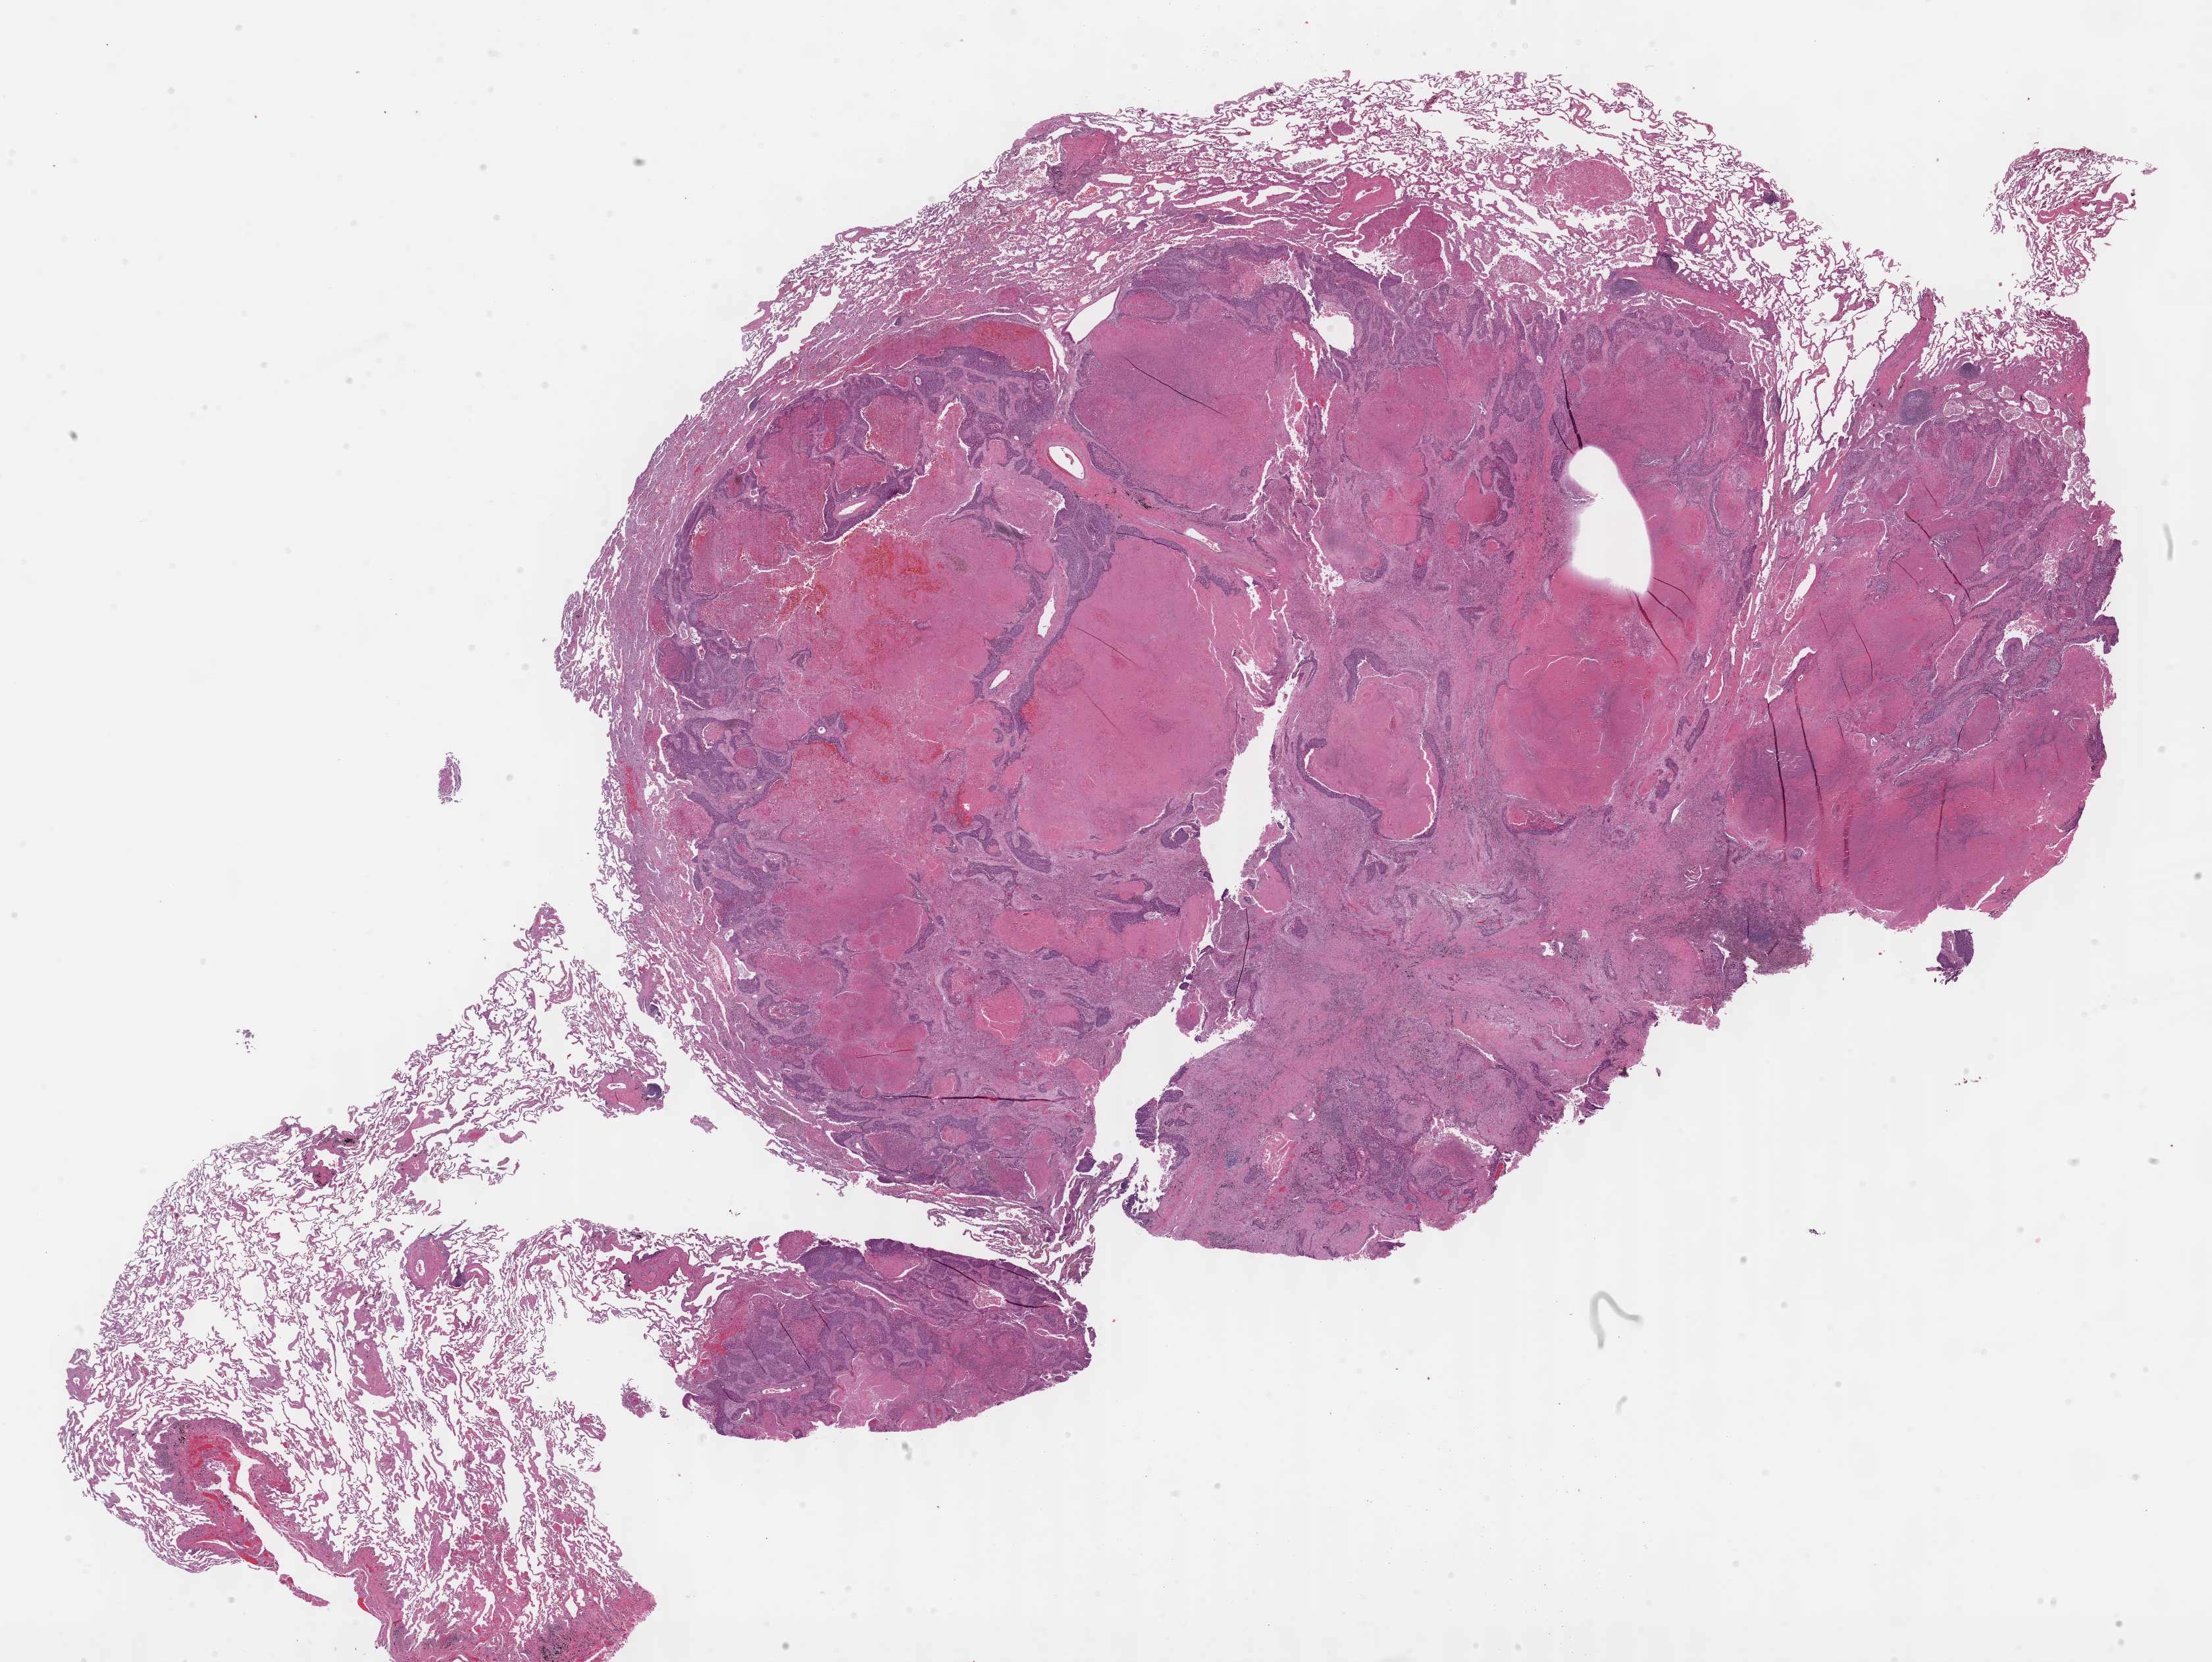
H&E-stained whole-slide image, whole scanned area (about 27.2 x 20.4 mm, from a 40x scan) shown as a low-resolution overview, FFPE section, sample: primary tumour, lung. Patient: male, age at initial diagnosis 61 years.
• histologic diagnosis: Squamous cell carcinoma, NOS
• laterality: left
• AJCC pathologic stage: IB